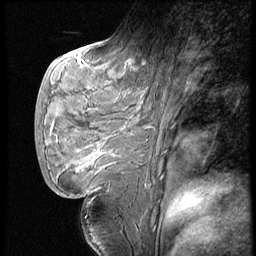
Breast MRI (dynamic contrast-enhanced), one sagittal slice; slice 23 of 62 in the series (ordered by position); dynamic contrast-enhanced series, image 2 of 4 at this slice position (ordered by acquisition); 1.5 T; TE 4.2 ms, TR 9 ms; 256 × 256 image matrix. Female patient, age 28 years. From the clinical record (not read from this slice): setting: breast cancer imaged before/during neoadjuvant chemotherapy.
Annotated regions visible in this slice (semi-automatically segmented with operator editing):
- analysis volume of interest (the breast-tissue region the enhancement analysis was run in; not a lesion): bounding box (x1, y1, x2, y2) in pixels: (42, 54, 150, 183)
- tumour enhancement mask (voxels above the 140 % enhancement threshold inside the analysis volume of interest): (52, 62, 145, 170)